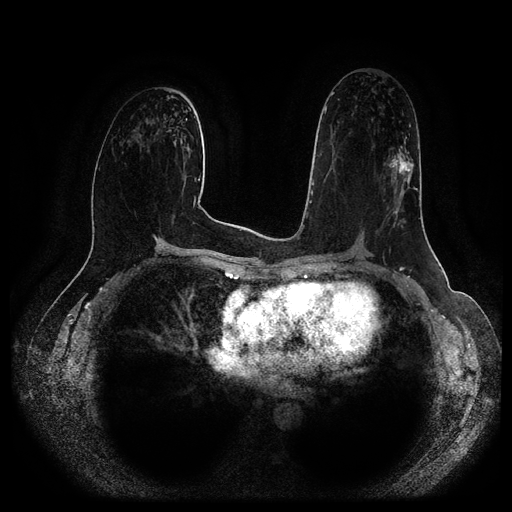
Breast MRI (dynamic contrast-enhanced, multi-phase), one axial slice. Position 55 of 116 along the scan axis. Dynamic contrast-enhanced series, time point 2 of 5 at this slice position (early post-contrast). 1.5 T. TE 2.6 ms, TR 5.2 ms. 2 mm slice thickness. 512 × 512 image matrix. Patient: female, 57 years.
Outlined on this slice (semi-automatically segmented with operator editing):
- breast lesion (labelled 'tumour' in the annotation; benign lesions carry a separate 'benign' label): bounding box <389,149,413,180> (left, top, right, bottom; pixels)